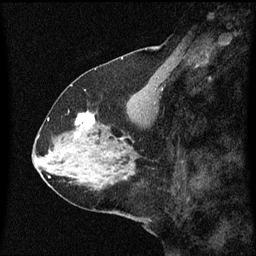
Breast MRI (dynamic contrast-enhanced), one sagittal slice. Position 27 of 60 along the scan axis. Dynamic contrast-enhanced series, image 2 of 3 at this slice position (ordered by acquisition). 1.5 T. TE 4.2 ms, TR 8.4 ms. 2 mm slice thickness. 256 × 256 image matrix, field of view 200 × 200 mm. Patient: female, 59 years.
Annotated regions visible in this slice (semi-automatically segmented with operator editing):
- analysis volume of interest (the breast-tissue region the enhancement analysis was run in; not a lesion): bounding box (x1, y1, x2, y2) in pixels: (70, 112, 99, 137)
- tumour enhancement mask (voxels above the 70 % enhancement threshold inside the analysis volume of interest): (76, 114, 96, 127)